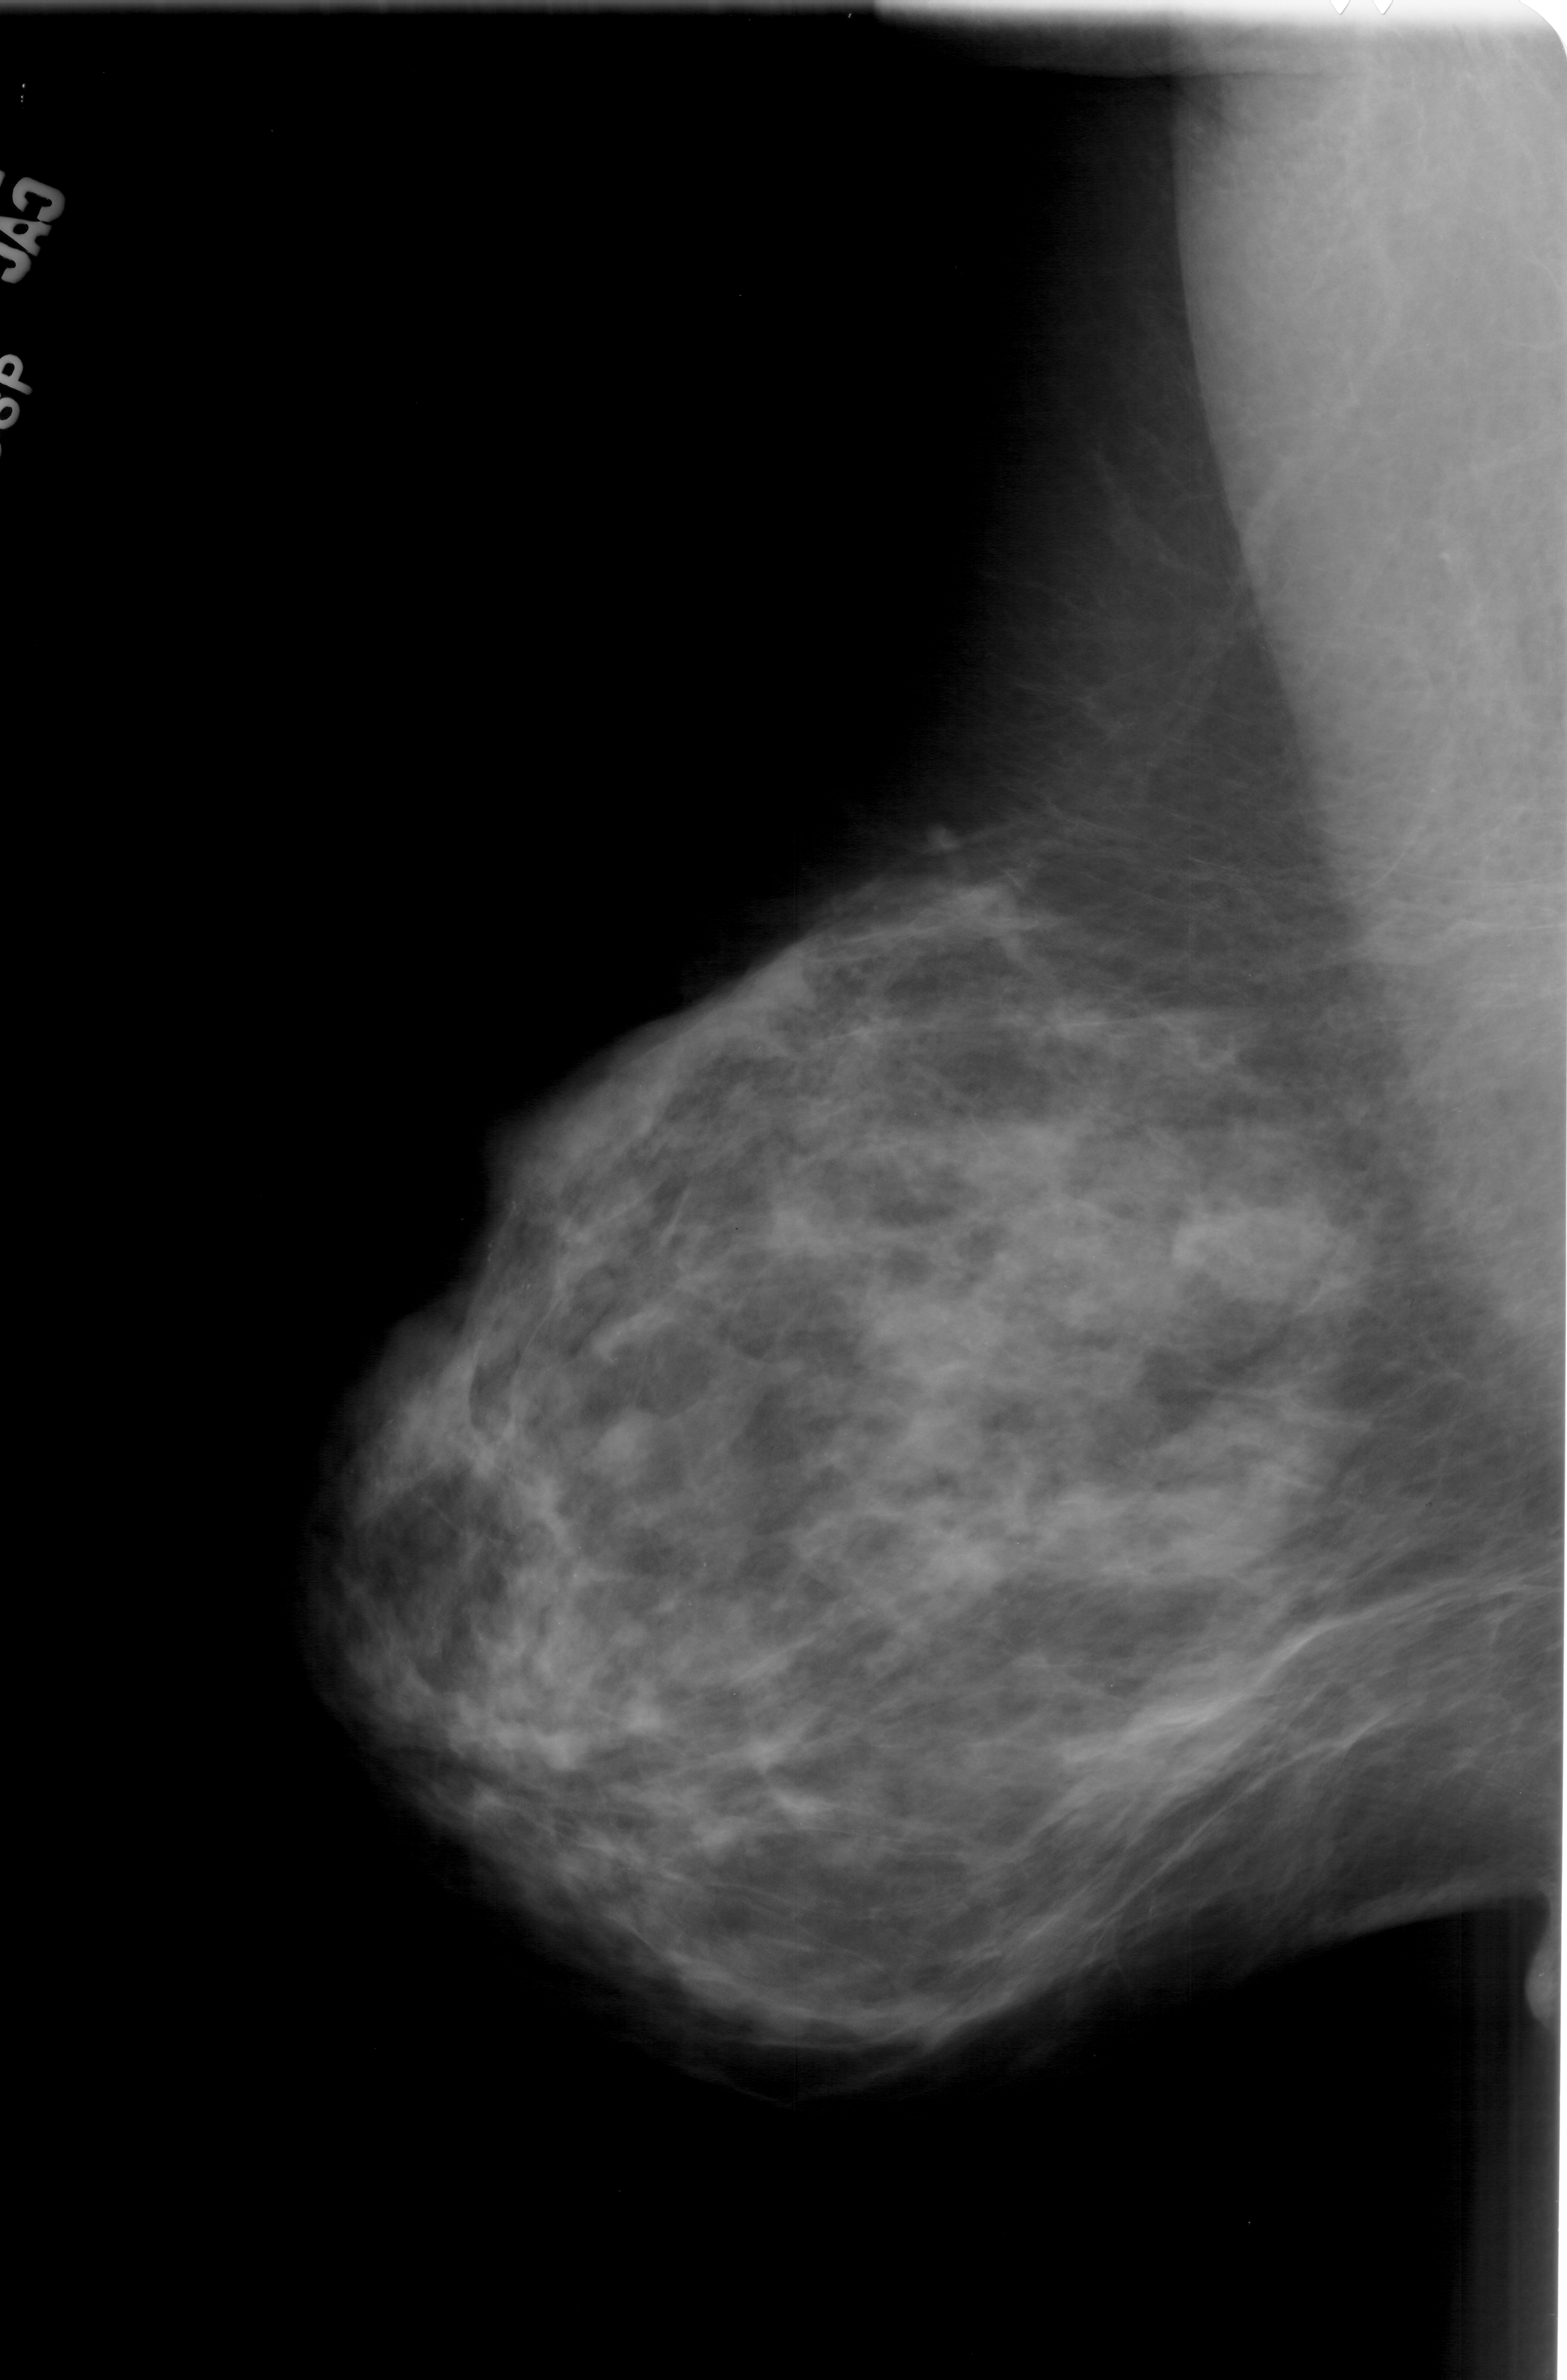
Digitized screen-film mammogram. Left breast. Mediolateral oblique (MLO) view. 1567 × 2380 image matrix.
Marked abnormalities (boxes around the expert regions of interest):
- calcifications, morphology pleomorphic, distribution segmental; BI-RADS assessment category 4; pathology (as recorded): malignant: box from (x=376, y=1151) to (x=742, y=1737) px